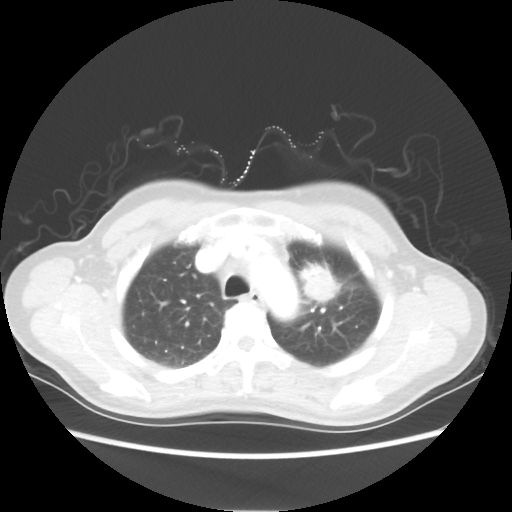
Chest CT, one axial slice. Slice 42 of 54 in the series (ordered by position). Lung window (W 1500 / L -600 HU). 512 × 512 image matrix, field of view 360 × 360 mm. Patient: female, 53 years. Case-level facts recorded for this patient, not image findings: clinical TNM (as recorded): T1c N0 M0.
Structures marked on this image (bounding box drawn by a radiologist):
- lung tumour (recorded histology: adenocarcinoma): box from (x=294, y=257) to (x=348, y=309) px
- lung tumour (recorded histology: adenocarcinoma): (x=298, y=265)–(x=345, y=306)